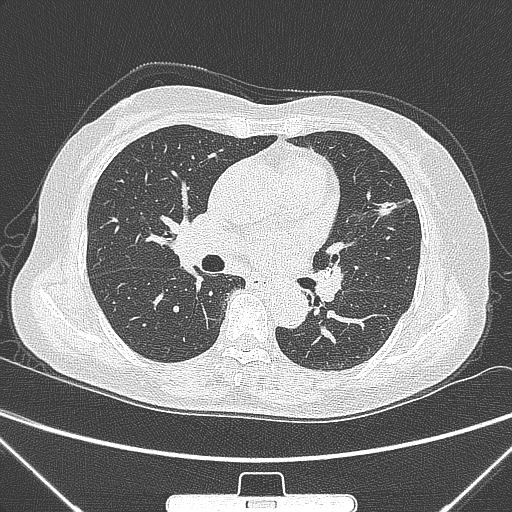
Chest CT, one axial slice; slice 151 of 300 in the series (ordered by position); lung window (W 1500 / L -600 HU); 1 mm slice thickness; 512 × 512 image matrix. Patient: female, 70 years. Case-level facts recorded for this patient, not image findings: clinical TNM (as recorded): T1b N0 M0.
Outlined on this slice (bounding box drawn by a radiologist):
- lung tumour (recorded histology: adenocarcinoma): bounding box (x1, y1, x2, y2) in pixels: (368, 192, 404, 230)